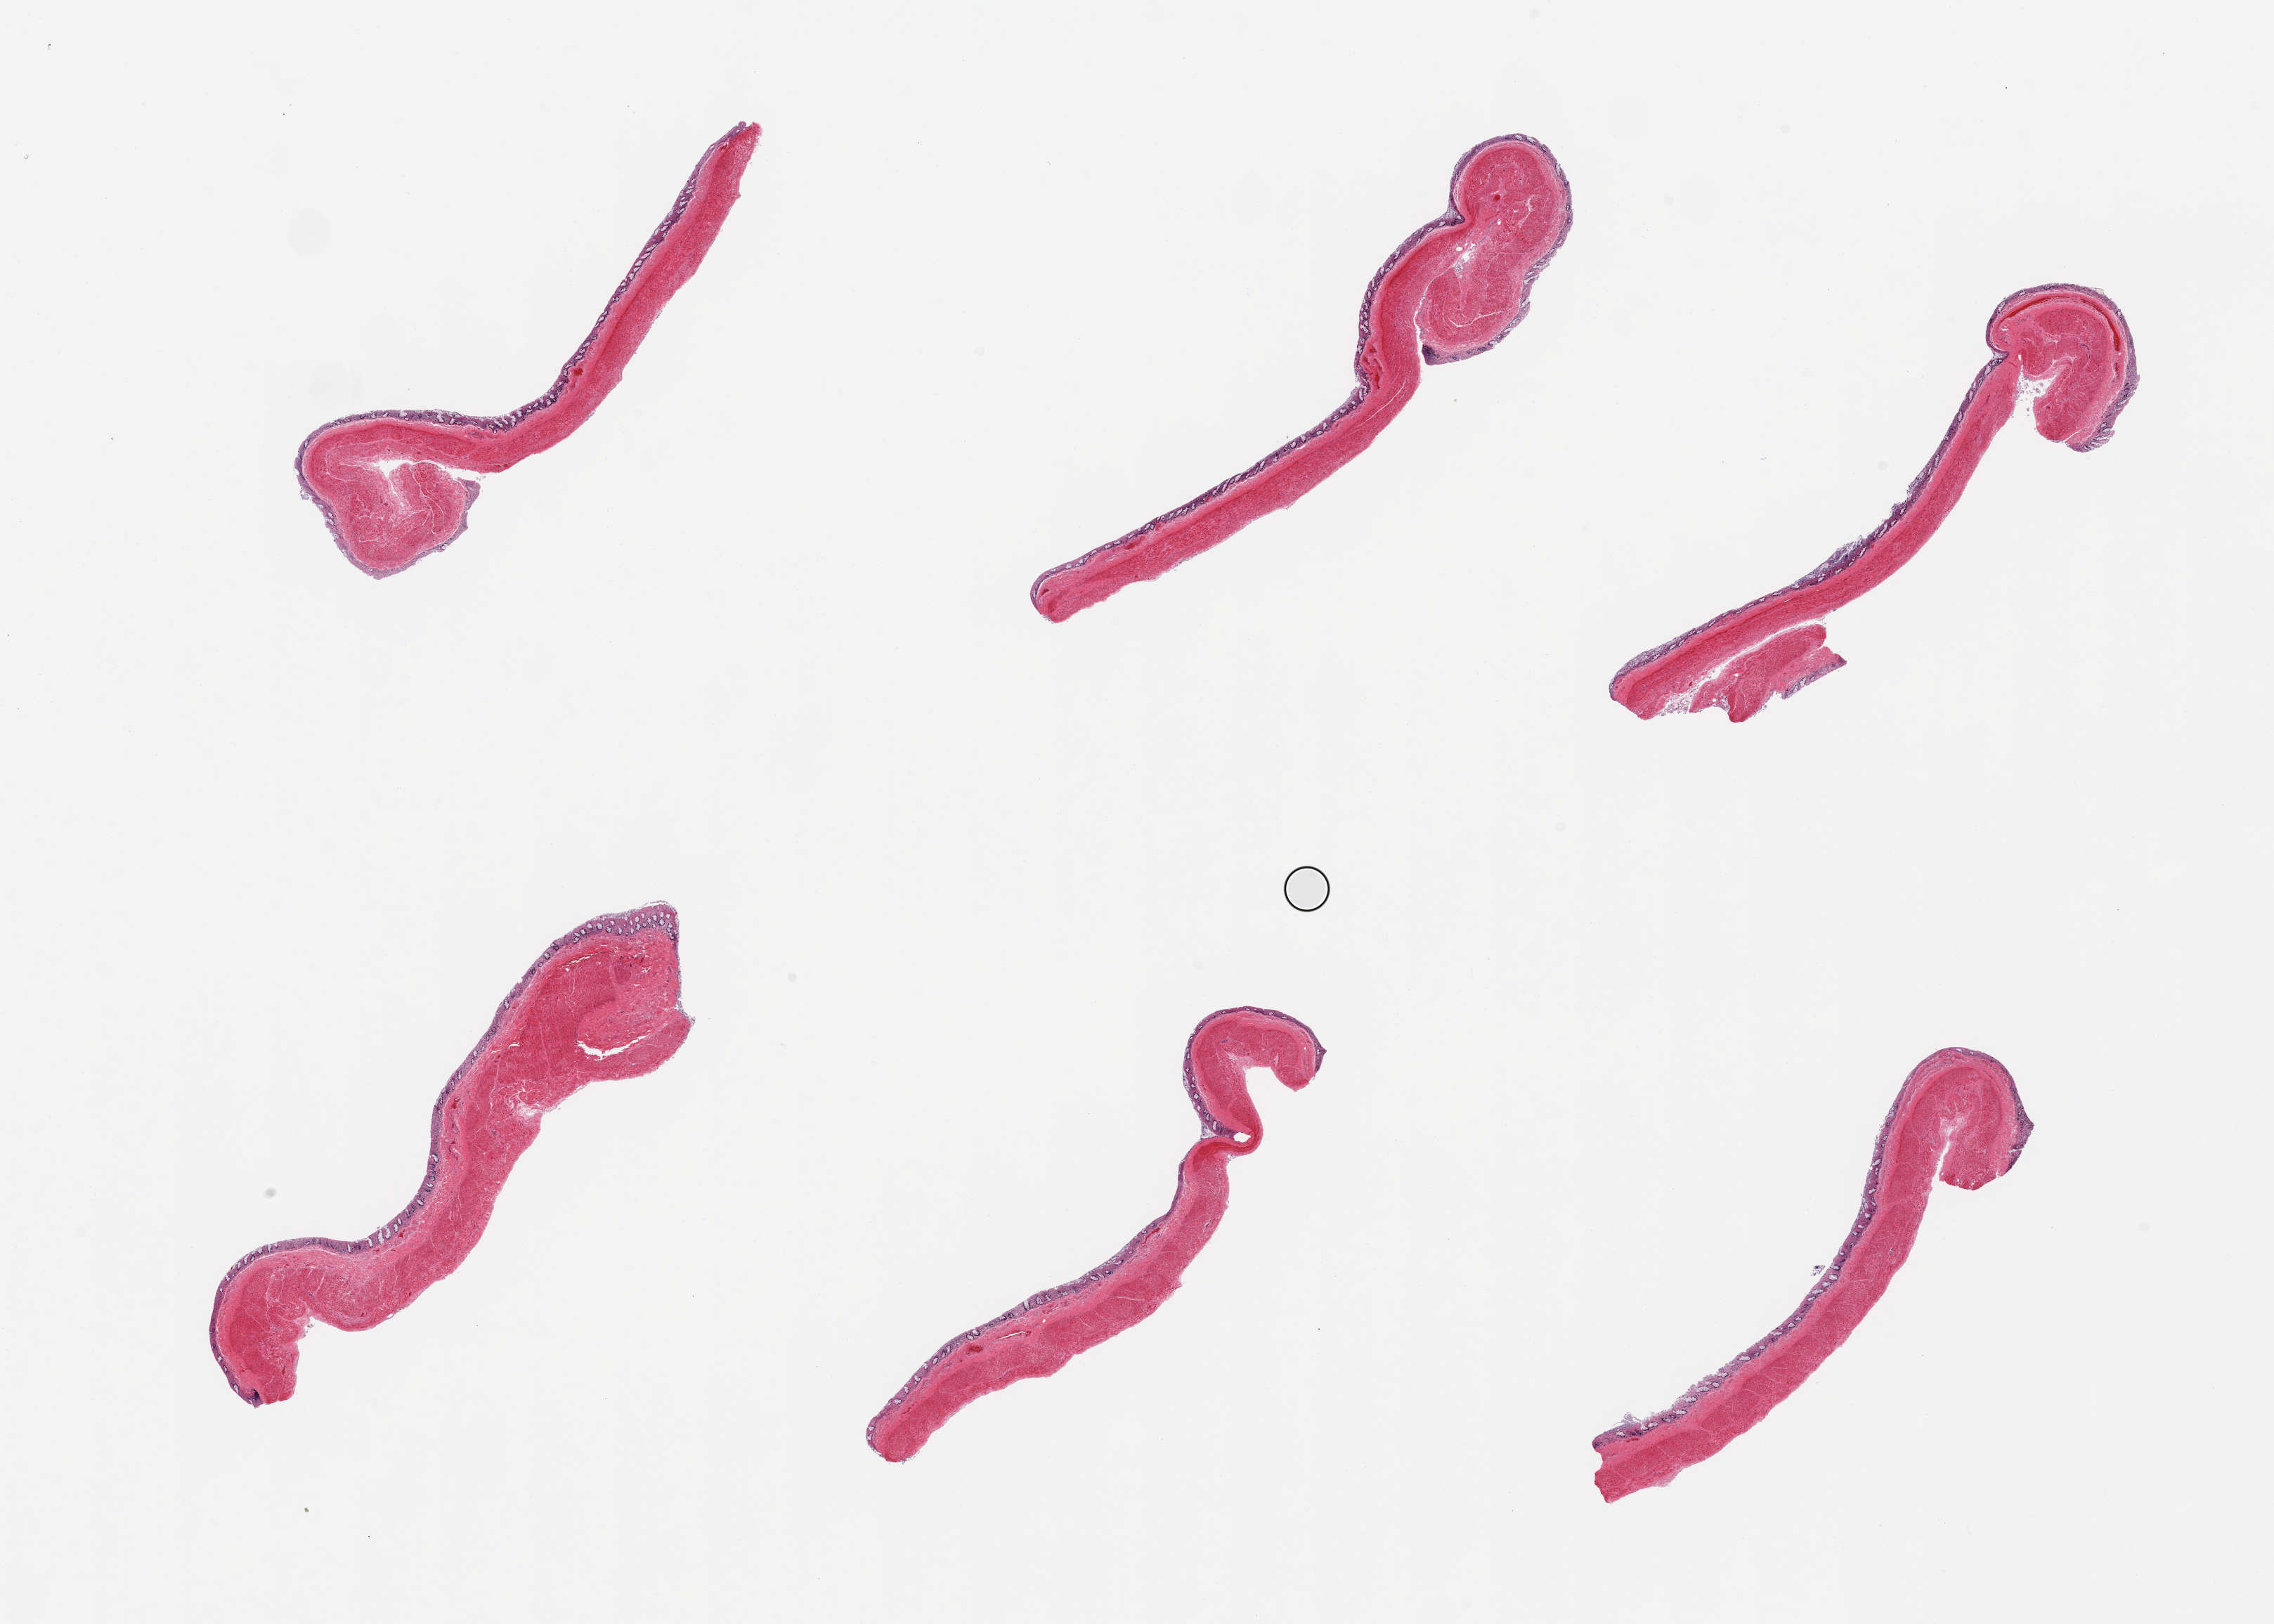
Digitized hematoxylin and eosin (H&E)-stained section, shown as a low-resolution overview of the whole scanned area (about 25.6 x 18.3 mm); PAXgene-fixed paraffin-embedded (PFPE) section; target tissue: transverse colon; donor tissue sample. Male donor.
Review note (as recorded): 6 pieces; full thickness, mucosa is largely autolyzed.